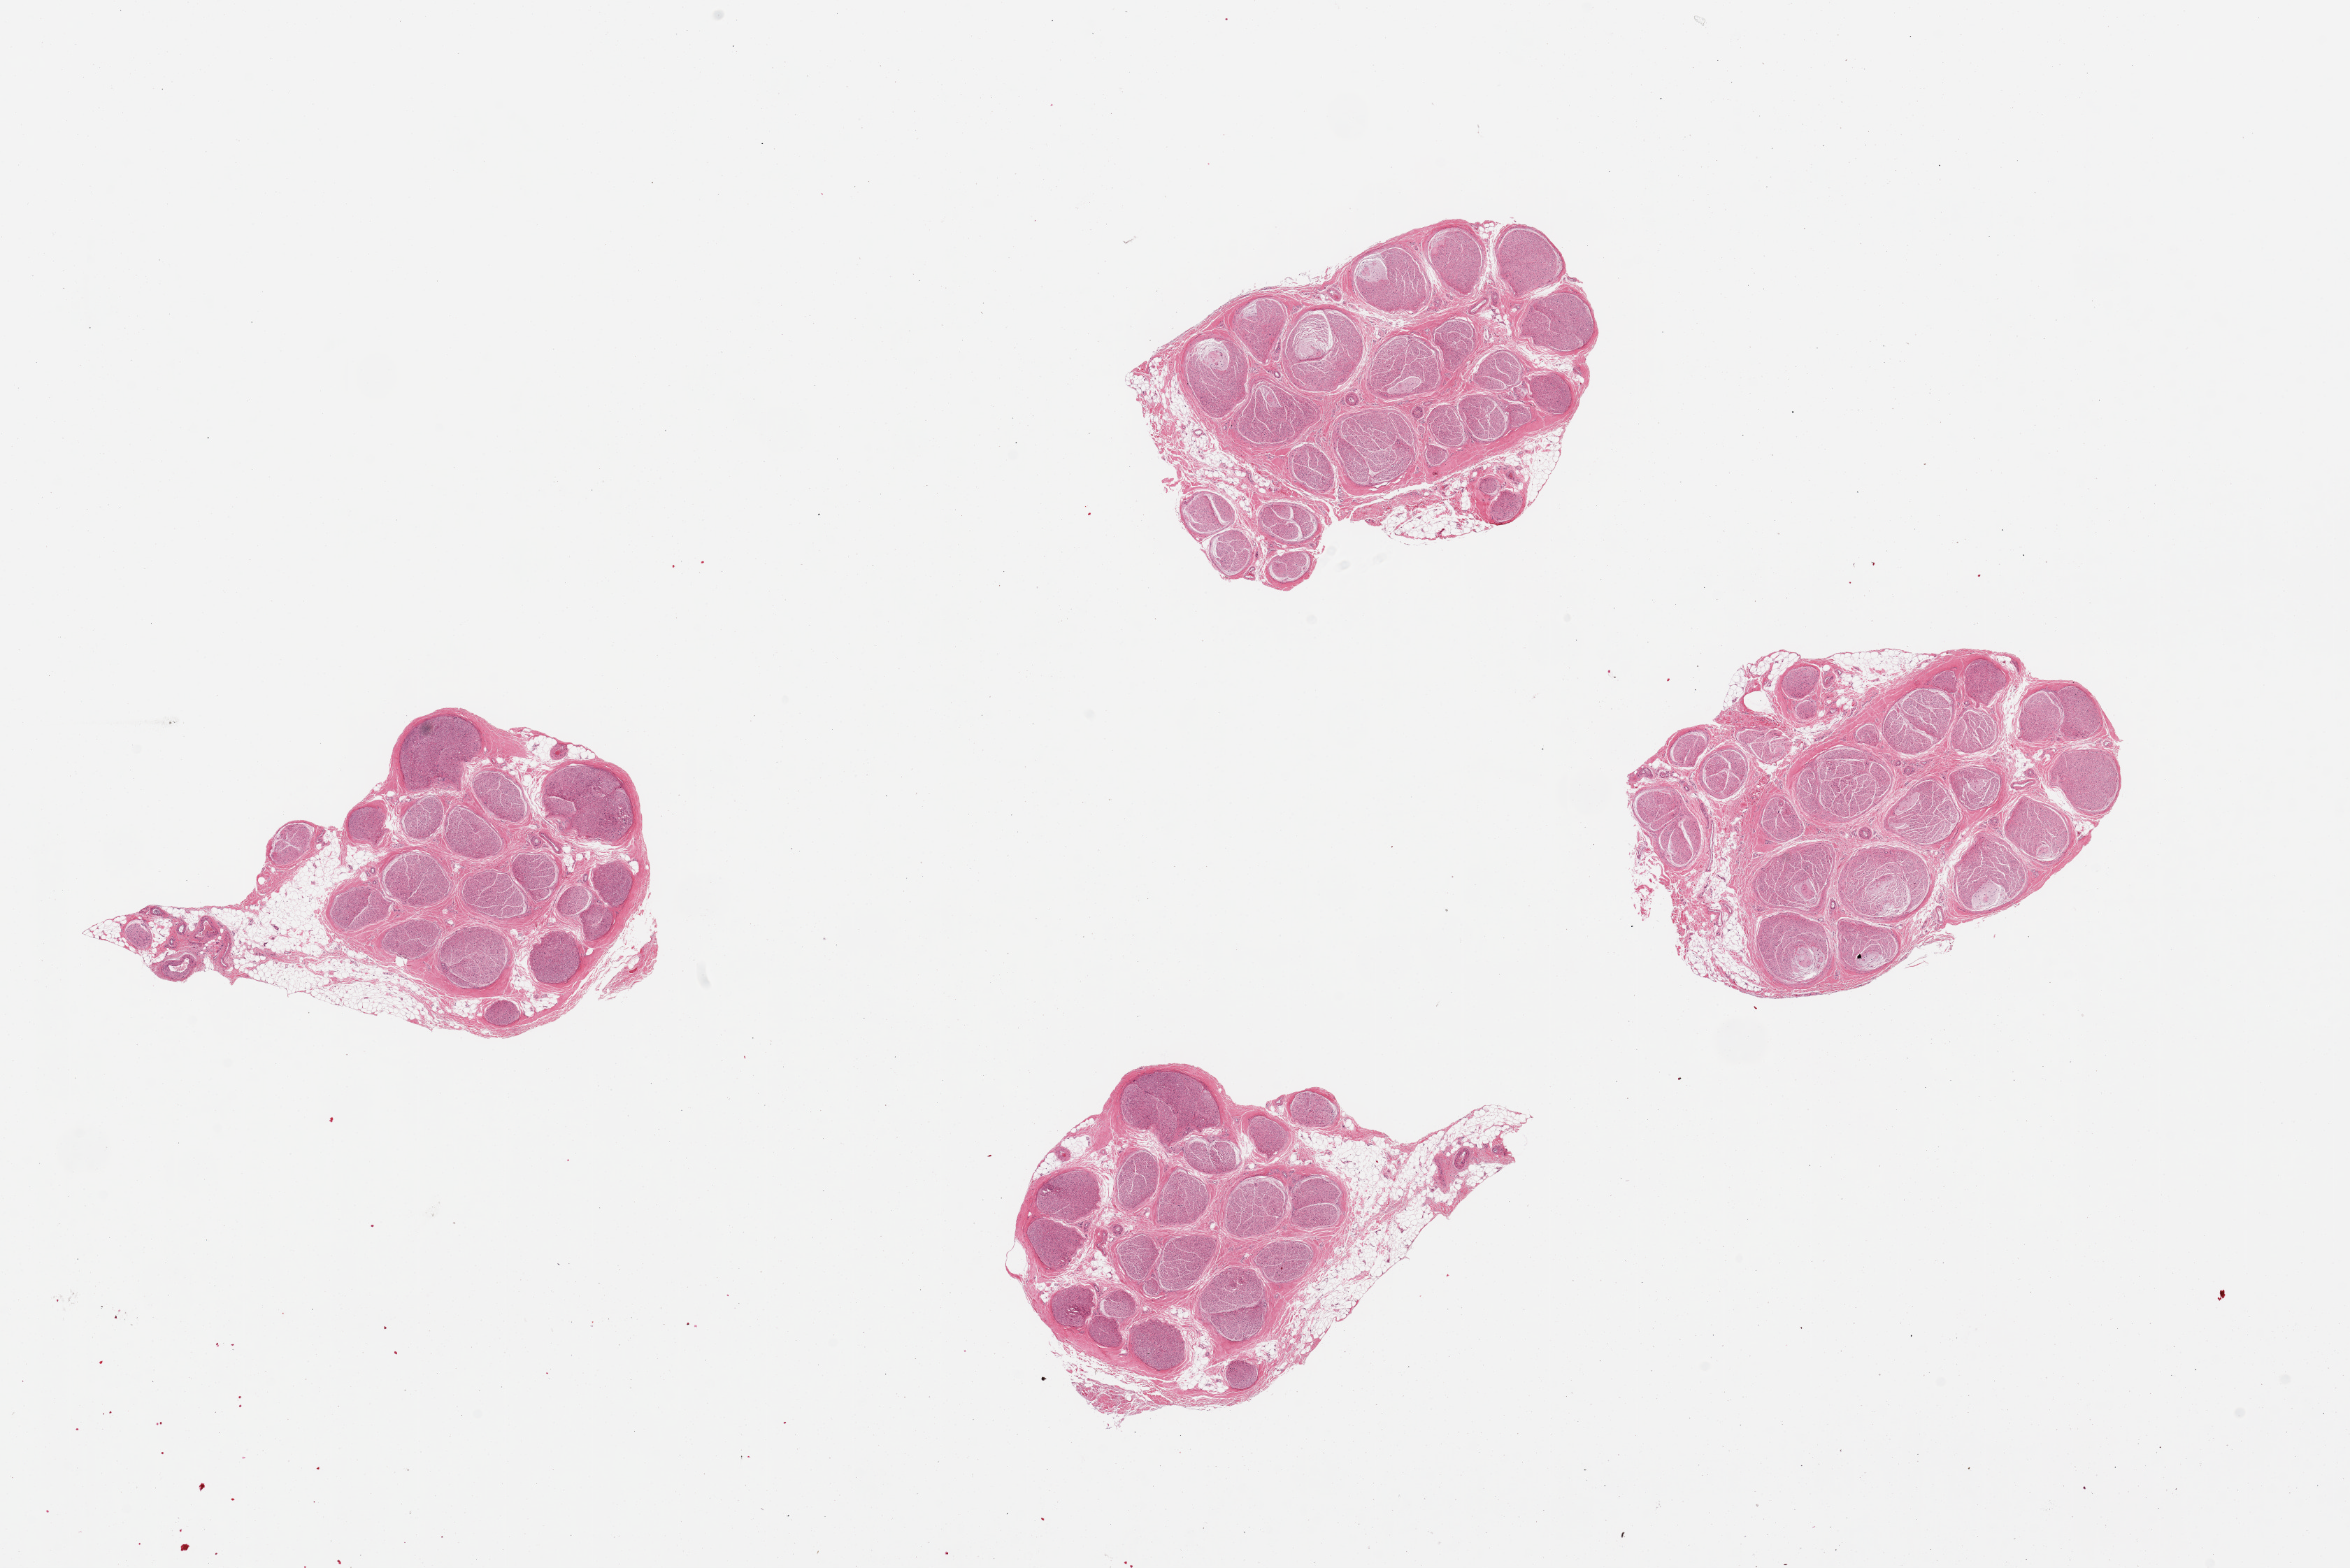
Whole-slide image, H&E stain — shown as a low-resolution overview of the whole scanned area (about 26.6 x 17.7 mm); PAXgene-fixed, paraffin-embedded tissue; section of tibial nerve (target tissue); donor tissue sample. Donor: male.
Reviewer comment on this tissue sample: 4 pieces; 10-20% external & internal fat.